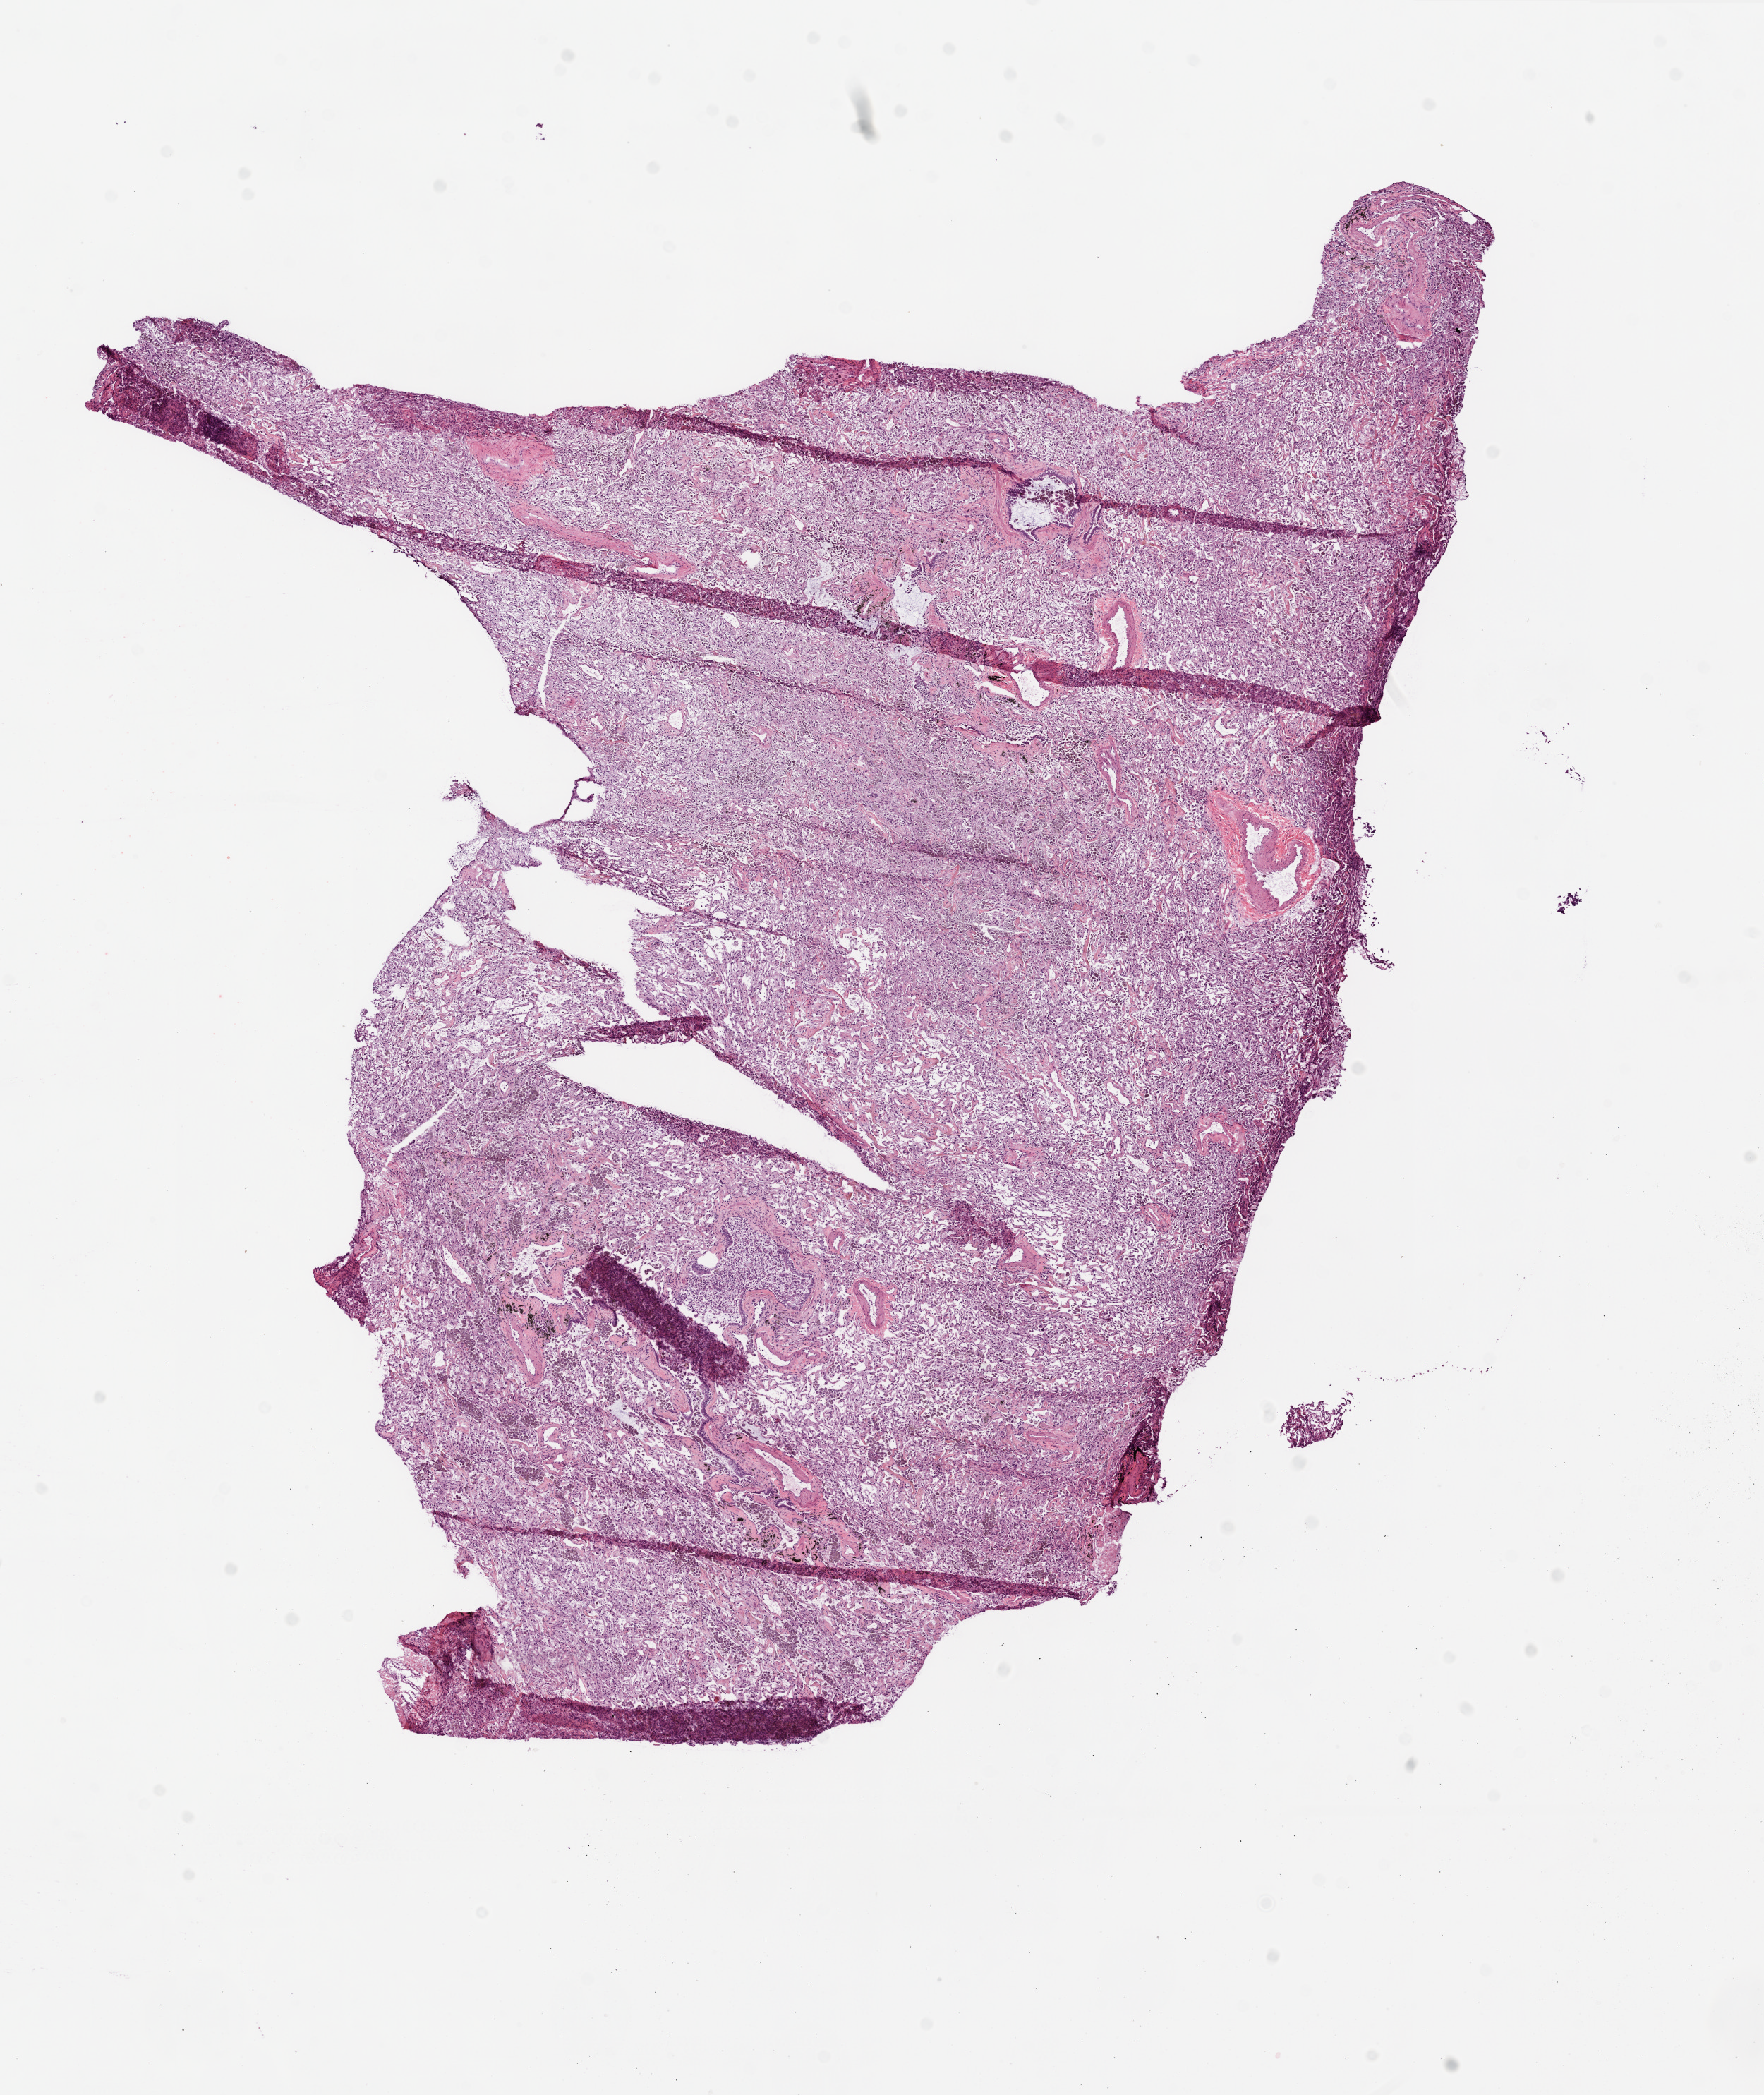
Whole-slide histology image, H&E — whole scanned area (about 10.0 x 11.9 mm, from a 20x scan) shown as a low-resolution overview, frozen section from the top of the tissue portion, lung, solid tissue normal (non-tumour tissue) sample. Patient: male, age at initial diagnosis 45 years.
- this section: solid tissue normal (non-tumour) sample from the same patient
- patient diagnosis: Adenocarcinoma, NOS (upper lobe, lung)